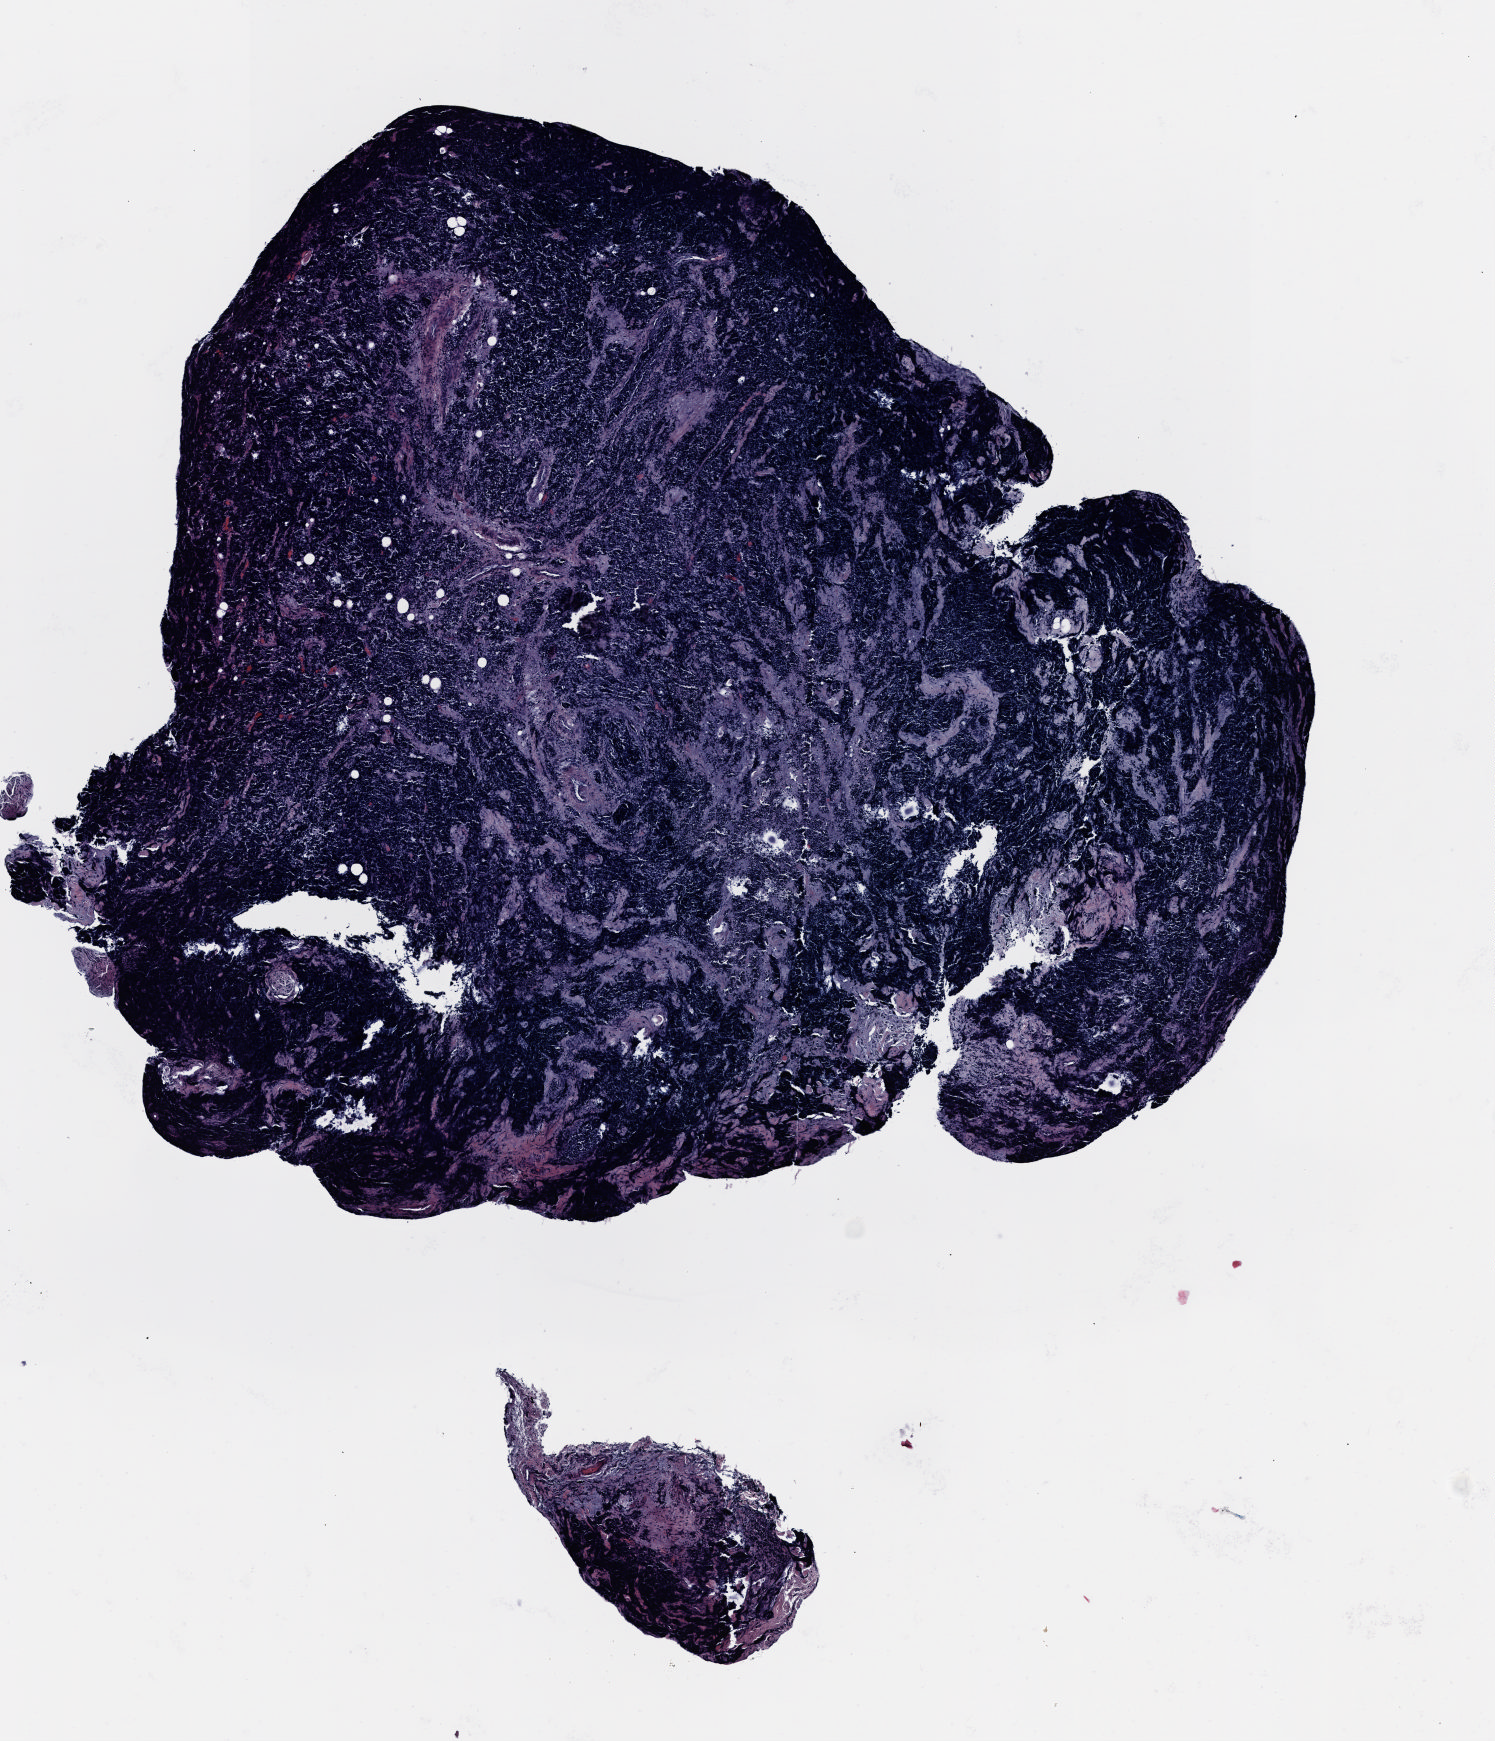
H&E whole-slide image — low-resolution overview of the scanned area, about 6.0 x 7.0 mm. FFPE section. Lung. Female, age 57 at enrolment. Current smoker at enrolment. Grade: cannot be assessed (GX).
* participant's lung-cancer diagnosis: Small cell carcinoma, NOS
* primary tumour location (clinical record): right middle lobe
* tumour size (pathology): 5 mm
* stage (AJCC 7th edition): IIIA